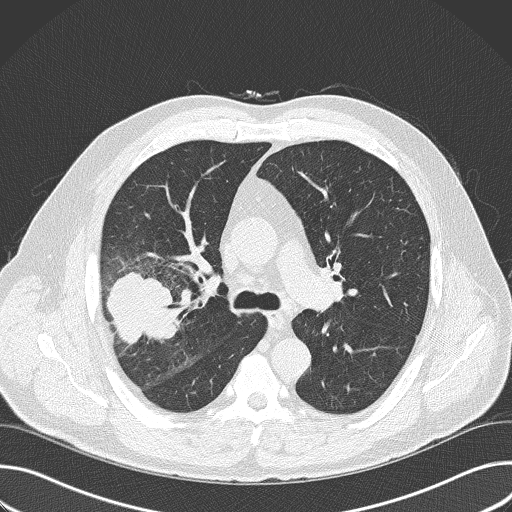
Low-dose screening chest CT, axial slice. Baseline annual screen. Lung window (W 1500 / L -600 HU). 2 mm slice thickness. Lung (sharp) reconstruction kernel (B50f). Slice 104 of 157 in the series. 512 × 512 image matrix. Male, age 56 years at enrolment. Current smoker at enrolment.
• Expert-annotated lung lesion, bounding box (x1, y1, x2, y2) in pixels: (82, 262, 187, 369).
• Screening reader's record for this exam (one nodule recorded; not confirmed to be the boxed lesion): non-calcified nodule or mass ≥4 mm, right upper lobe, 6 × 5 mm, spiculated (stellate) margins, soft tissue attenuation.
• Participant outcome: lung cancer diagnosed 16 days after this screen — adenocarcinoma, NOS, right upper lobe, poorly differentiated (G3), stage IIB (AJCC 6th edition), 60 mm at pathology.